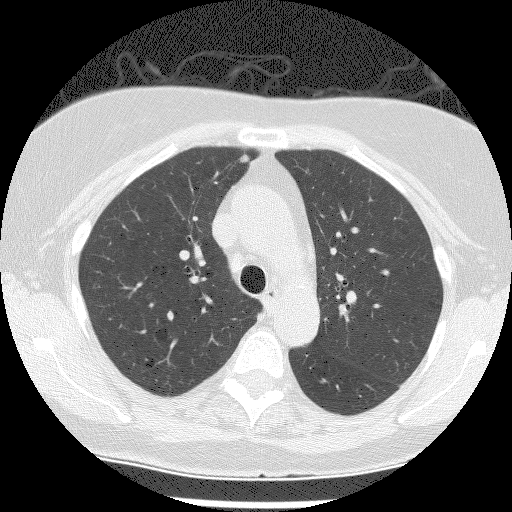
Low-dose screening chest CT, one axial slice; slice 104 of 149 in the series (ordered by position); reconstruction kernel BONE; 120 kVp; lung window (W 1500 / L -600 HU); 2.5 mm slice thickness; 512 × 512 image matrix.
Outlined on this slice (outlined manually by an expert reader):
- lesion 1 (tumor, upper lobe of right lung): box from (x=238, y=152) to (x=250, y=163) px